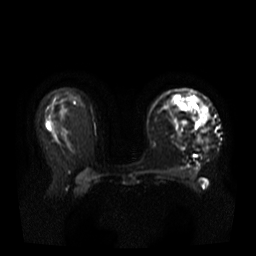
Breast MRI, one axial slice; position 23 of 37 along the scan axis; diffusion-weighted series; image 2 of 4 stored at this slice position (different b-values; order by instance number); 3 T; 5 mm slice thickness; 256 × 256 image matrix. Female patient.
Annotated regions visible in this slice (outlined manually by an expert reader):
- tumour on diffusion-weighted imaging: bounding box [x1, y1, x2, y2] px = [194, 109, 210, 144]